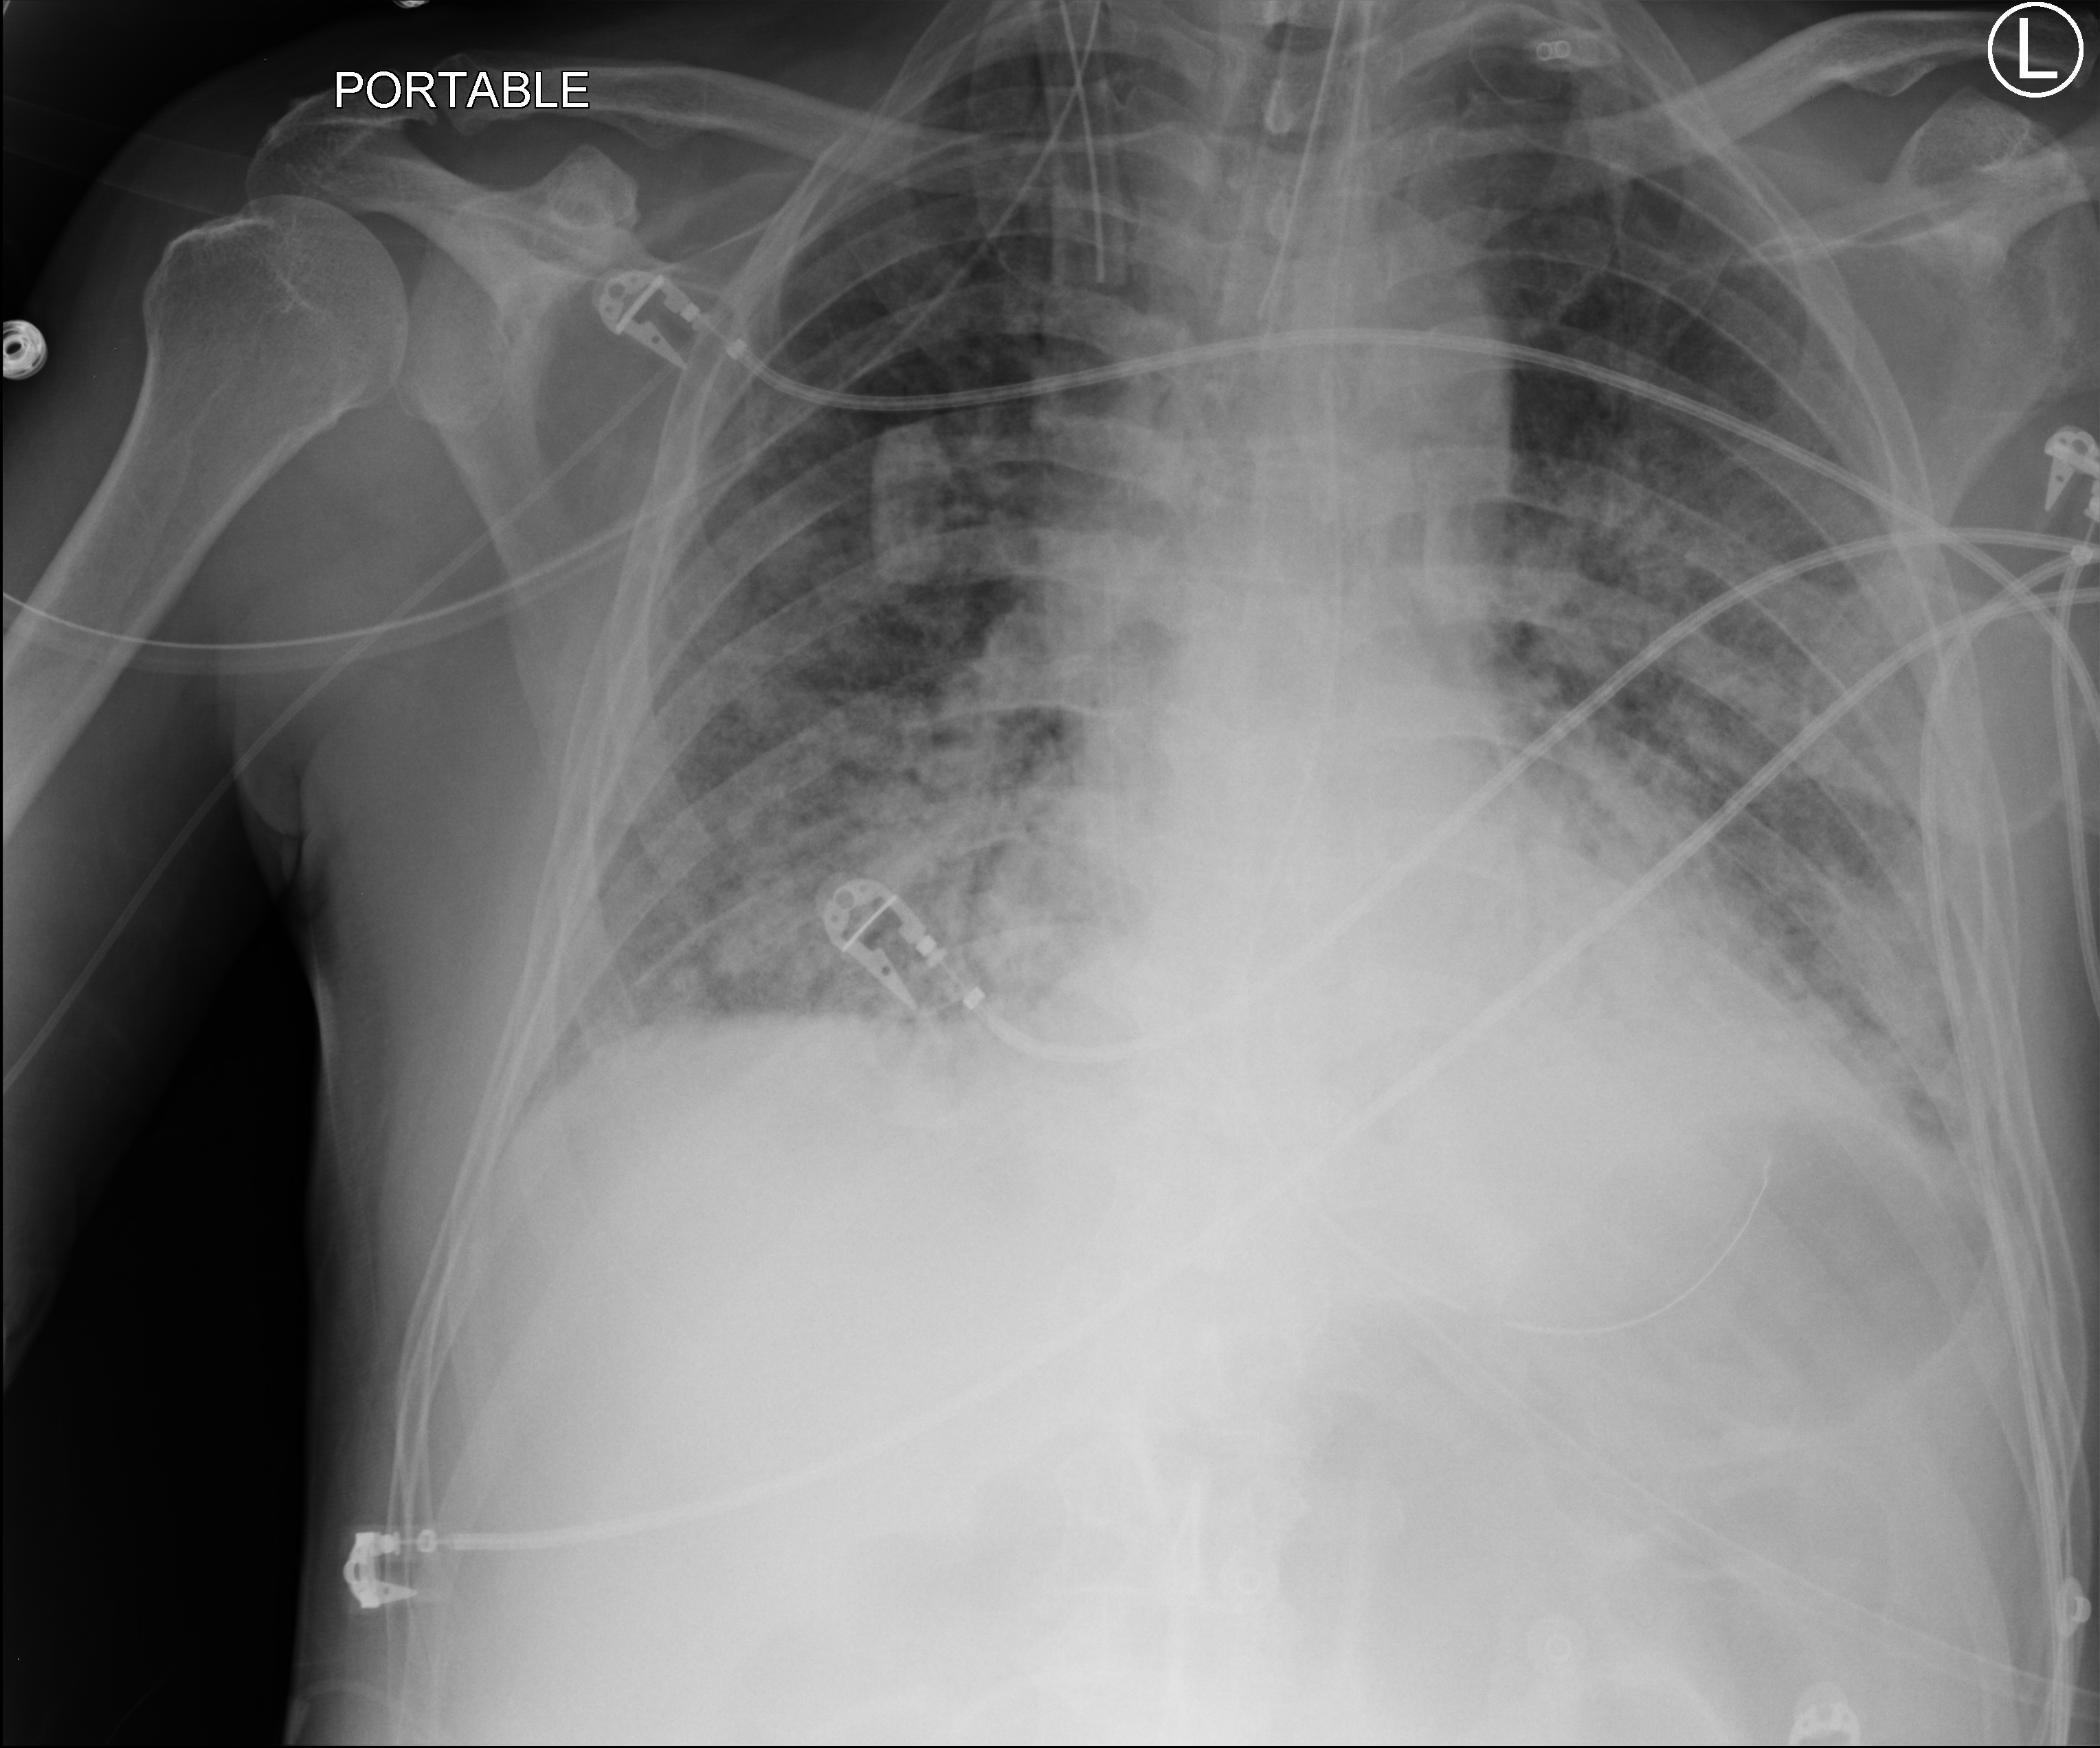
Portable chest radiograph; anteroposterior (AP) projection. Male patient hospitalised with COVID-19, age 60–74 years.
Admission-level facts for this patient (not findings on this image; timing relative to this image not recorded):
- mechanically ventilated during this hospital stay: yes